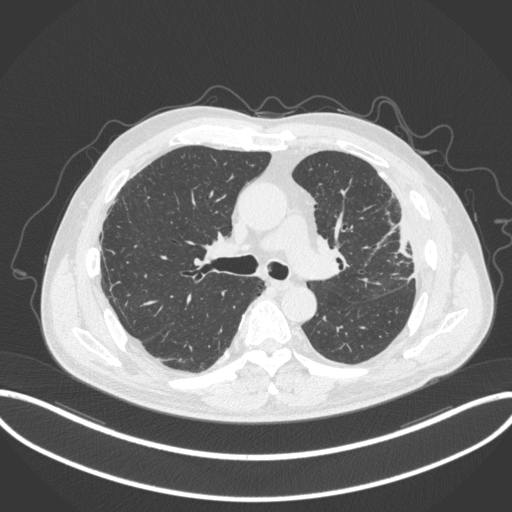
Chest CT, one axial slice; position 215 of 382 along the scan axis; reconstruction kernel B31f; 120 kVp; lung window (W 1500 / L -600 HU); 1 mm slice thickness; 512 × 512 image matrix, field of view 415 × 415 mm. Patient: male, 64 years. Case-level facts recorded for this patient, not image findings: clinical TNM (as recorded): T4 N1 M0; histopathological grade: G3.
Structures marked on this image (rectangle marked by the reading radiologist):
- lung tumour (recorded histology: adenocarcinoma): bounding box (x1, y1, x2, y2) in pixels: (387, 215, 415, 261)